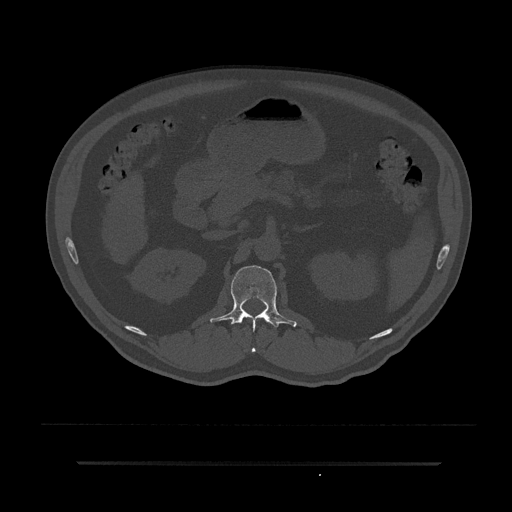
CT including the spine, one axial slice; reconstruction kernel Br40s/3; bone window (W 1800 / L 400 HU); 0.5 mm slice thickness; 512 × 512 image matrix. Patient: male, 59 years. From the clinical record (not read from this slice): primary cancer: bile ducts.
Annotated regions visible in this slice (semi-automatic segmentation, software-assisted and operator-edited):
- L1 vertebra: bounding box [x1, y1, x2, y2] px = [210, 265, 297, 352]